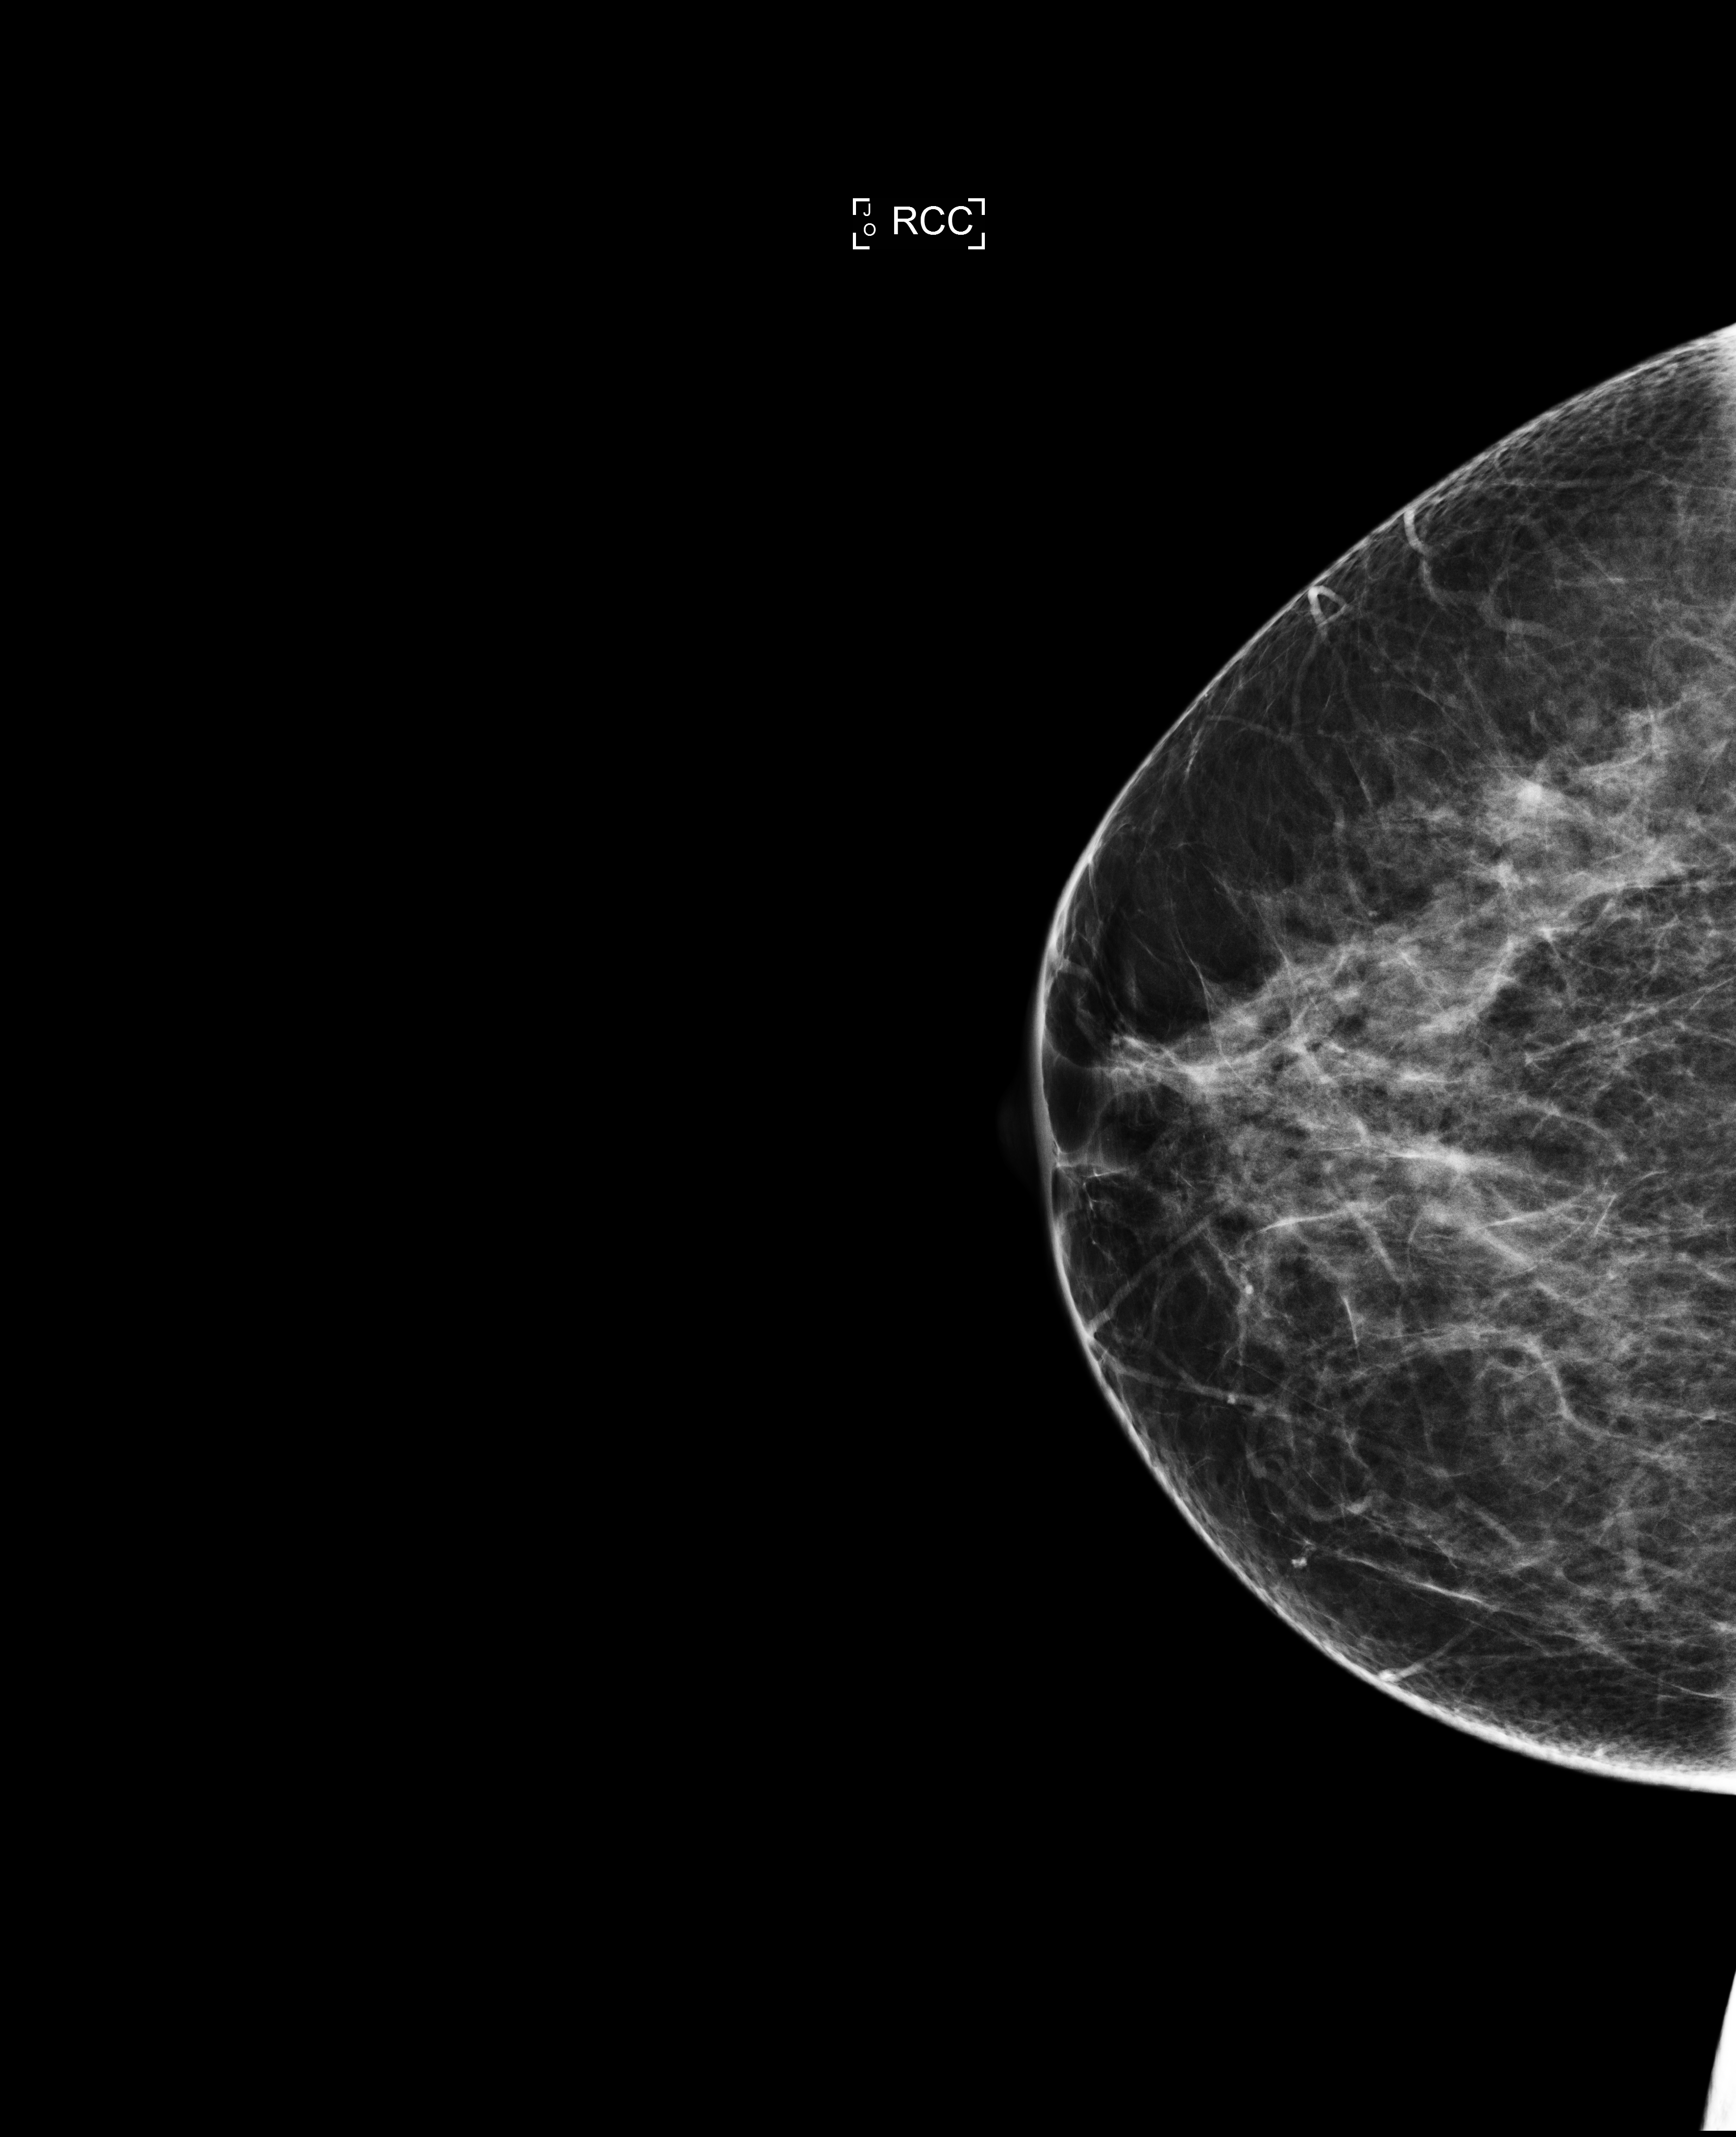
Annual screening mammography examination. Patient aged 48 years (female).
Image type: full-field digital mammogram. Breast: right. Projection: CC view.